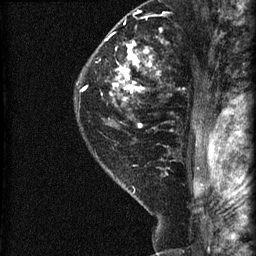
Breast MRI (dynamic contrast-enhanced), one sagittal slice. Position 50 of 60 along the scan axis. Dynamic contrast-enhanced series, image 2 of 3 at this slice position (ordered by acquisition). 1.5 T. TE 4.2 ms, TR 22.7 ms. 1.8 mm slice thickness. 256 × 256 image matrix, field of view 180 × 180 mm. Patient: female, 45 years. From the clinical record (not read from this slice): setting: breast cancer imaged before/during neoadjuvant chemotherapy; receptor status: HR-positive, HER2-negative.
Structures marked on this image (semi-automatic segmentation, software-assisted and operator-edited):
- analysis volume of interest (the breast-tissue region the enhancement analysis was run in; not a lesion): bounding box (x1, y1, x2, y2) in pixels: (74, 11, 205, 140)
- tumour enhancement mask (voxels above the 90 % enhancement threshold inside the analysis volume of interest): (80, 40, 160, 127)